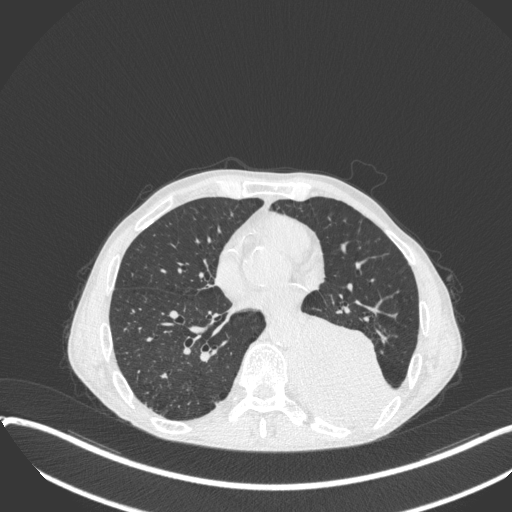
Chest CT, one axial slice. Position 152 of 400 along the scan axis. 120 kVp. Lung window (W 1500 / L -600 HU). 512 × 512 image matrix, field of view 400 × 400 mm. Patient: male, 57 years. Case-level facts recorded for this patient, not image findings: clinical TNM (as recorded): T4 N0 M0.
Annotated regions visible in this slice (bounding box drawn by a radiologist):
- lung tumour (recorded histology: squamous cell carcinoma): bounding box (x1, y1, x2, y2) in pixels: (294, 307, 393, 436)